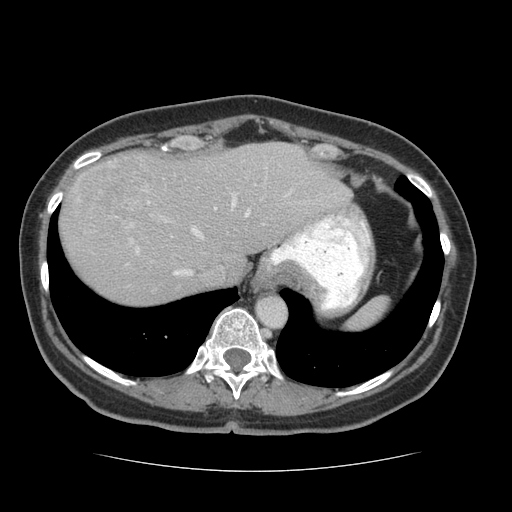
Contrast-enhanced abdominal CT (liver protocol), one axial slice. Position 56 of 75 along the scan axis. Soft-tissue window (W 400 / L 40 HU). 512 × 512 image matrix, field of view 360 × 360 mm. Case-level facts recorded for this patient, not image findings: diagnosis: hepatocellular carcinoma (patient treated with transarterial chemoembolisation; whether this scan precedes or follows treatment is not stated here); TNM stage (as recorded): Stage-I; Child-Pugh class: A; tumour nodularity: uninodular.
Outlined on this slice (semi-automatic segmentation, software-assisted and operator-edited):
- abdominal aorta: bounding box [x1, y1, x2, y2] px = [257, 296, 286, 327]
- liver parenchyma outside the tumour (the mass and vessels are separate outlines, so this box may not span the whole liver): [60, 142, 352, 304]
- mass: [76, 157, 156, 235]
- liver vessels: [130, 189, 293, 276]